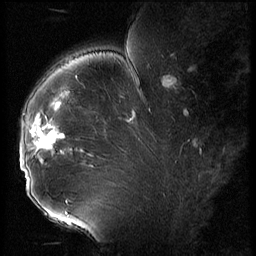
Breast MRI (dynamic contrast-enhanced), one sagittal slice. Slice 40 of 56 in the series (ordered by position). 3 images stored at this slice position (order not interpretable as contrast timing). 1.5 T. TE 4.2 ms, TR 9 ms. 2.5 mm slice thickness. 256 × 256 image matrix. Patient: female, 43 years. Case-level facts recorded for this patient, not image findings: setting: breast cancer imaged before/during neoadjuvant chemotherapy; receptor status: HER2-positive.
Structures marked on this image (semi-automatic segmentation, software-assisted and operator-edited):
- analysis volume of interest (the breast-tissue region the enhancement analysis was run in; not a lesion): bounding box [x1, y1, x2, y2] px = [20, 92, 74, 211]
- tumour enhancement mask (voxels above the 140 % enhancement threshold inside the analysis volume of interest): [21, 129, 65, 172]